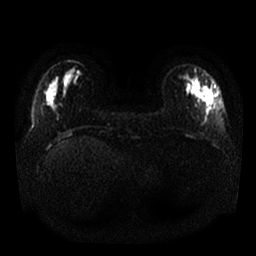
Breast MRI, one axial slice. Position 5 of 25 along the scan axis. Diffusion-weighted series; image 2 of 4 stored at this slice position (different b-values; order by instance number). 1.5 T. 4 mm slice thickness. 256 × 256 image matrix. Female patient.
Outlined on this slice (outlined manually by an expert reader):
- tumour on diffusion-weighted imaging: box from (x=190, y=79) to (x=215, y=118) px